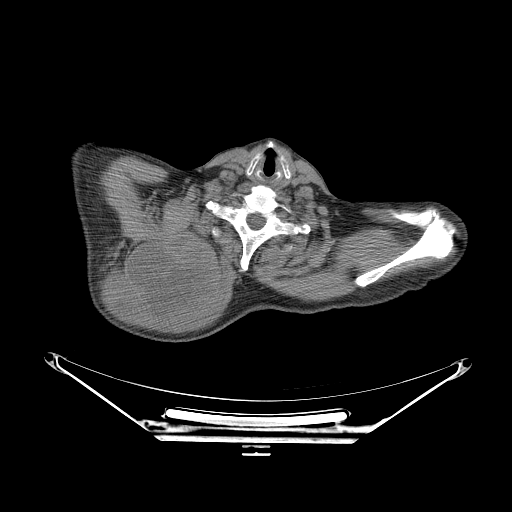
CT of an extremity soft-tissue mass (from a PET/CT study), one axial slice; position 212 of 267 along the scan axis; soft-tissue window (W 400 / L 40 HU); 3.75 mm slice thickness; 512 × 512 image matrix, field of view 500 × 500 mm. Male patient. Case-level facts recorded for this patient, not image findings: histological type: pleiomorphic spindle cell undifferentiated; grade: high; site of the primary tumour: right parascapusular.
Outlined on this slice (expert contour drawn on MRI and transferred to this co-registered scan by the dataset authors):
- gross tumour volume including surrounding oedema: bounding box (x1, y1, x2, y2) in pixels: (101, 230, 232, 323)
- gross tumour volume (mass): (128, 237, 216, 318)